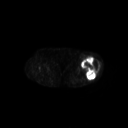
FDG PET of an extremity soft-tissue mass (from a PET/CT study), one axial slice. 3.27 mm slice thickness. 128 × 128 image matrix, field of view 700 × 700 mm. Female patient, age 62 years. From the clinical record (not read from this slice): histological type: undifferentiated – high grade; grade: high; site of the primary tumour: left thigh.
Outlined on this slice (expert contour drawn on MRI and transferred to this co-registered scan by the dataset authors):
- gross tumour volume including surrounding oedema: bounding box [x1, y1, x2, y2] px = [81, 56, 100, 79]
- gross tumour volume (mass): [81, 56, 99, 79]